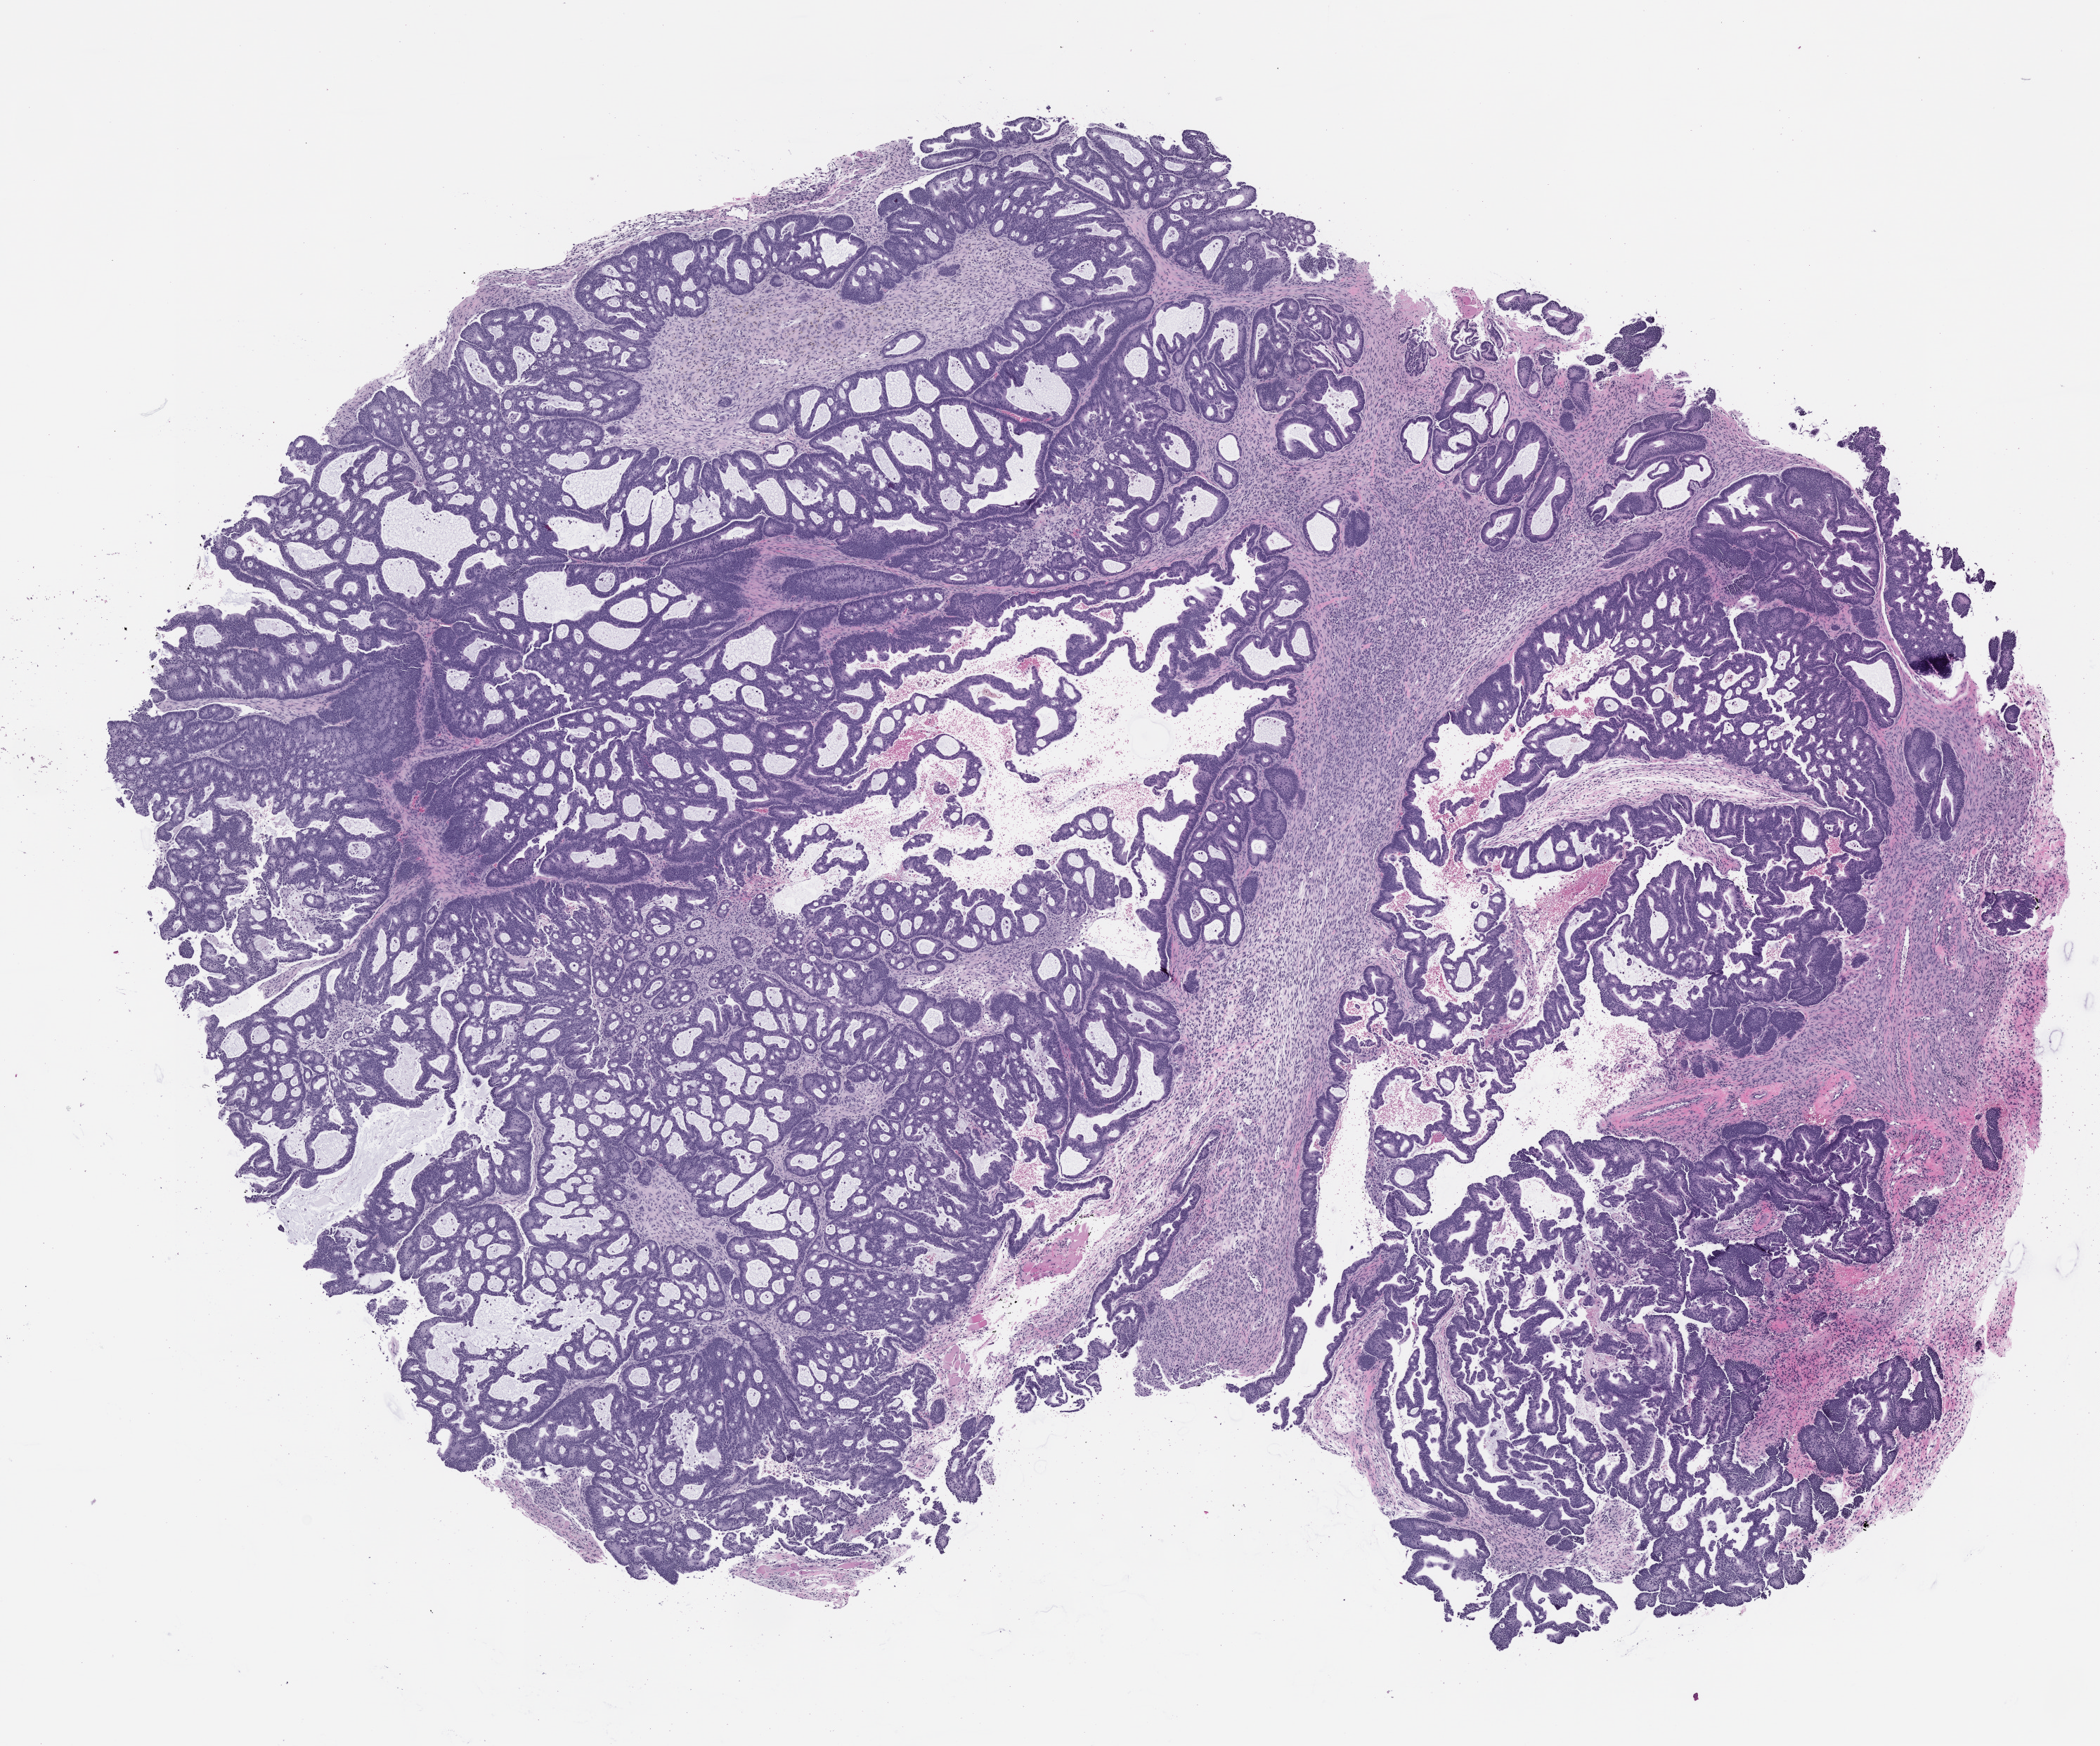
Whole-slide image, H&E: patient-derived xenograft (human tumor grown in a mouse), passage 2, a low-resolution overview of the entire scanned area, about 12.0 x 10.0 mm; formalin-fixed paraffin-embedded section; originating tumor site category: colon.
- originating patient diagnosis: Colon Adenocarcinoma